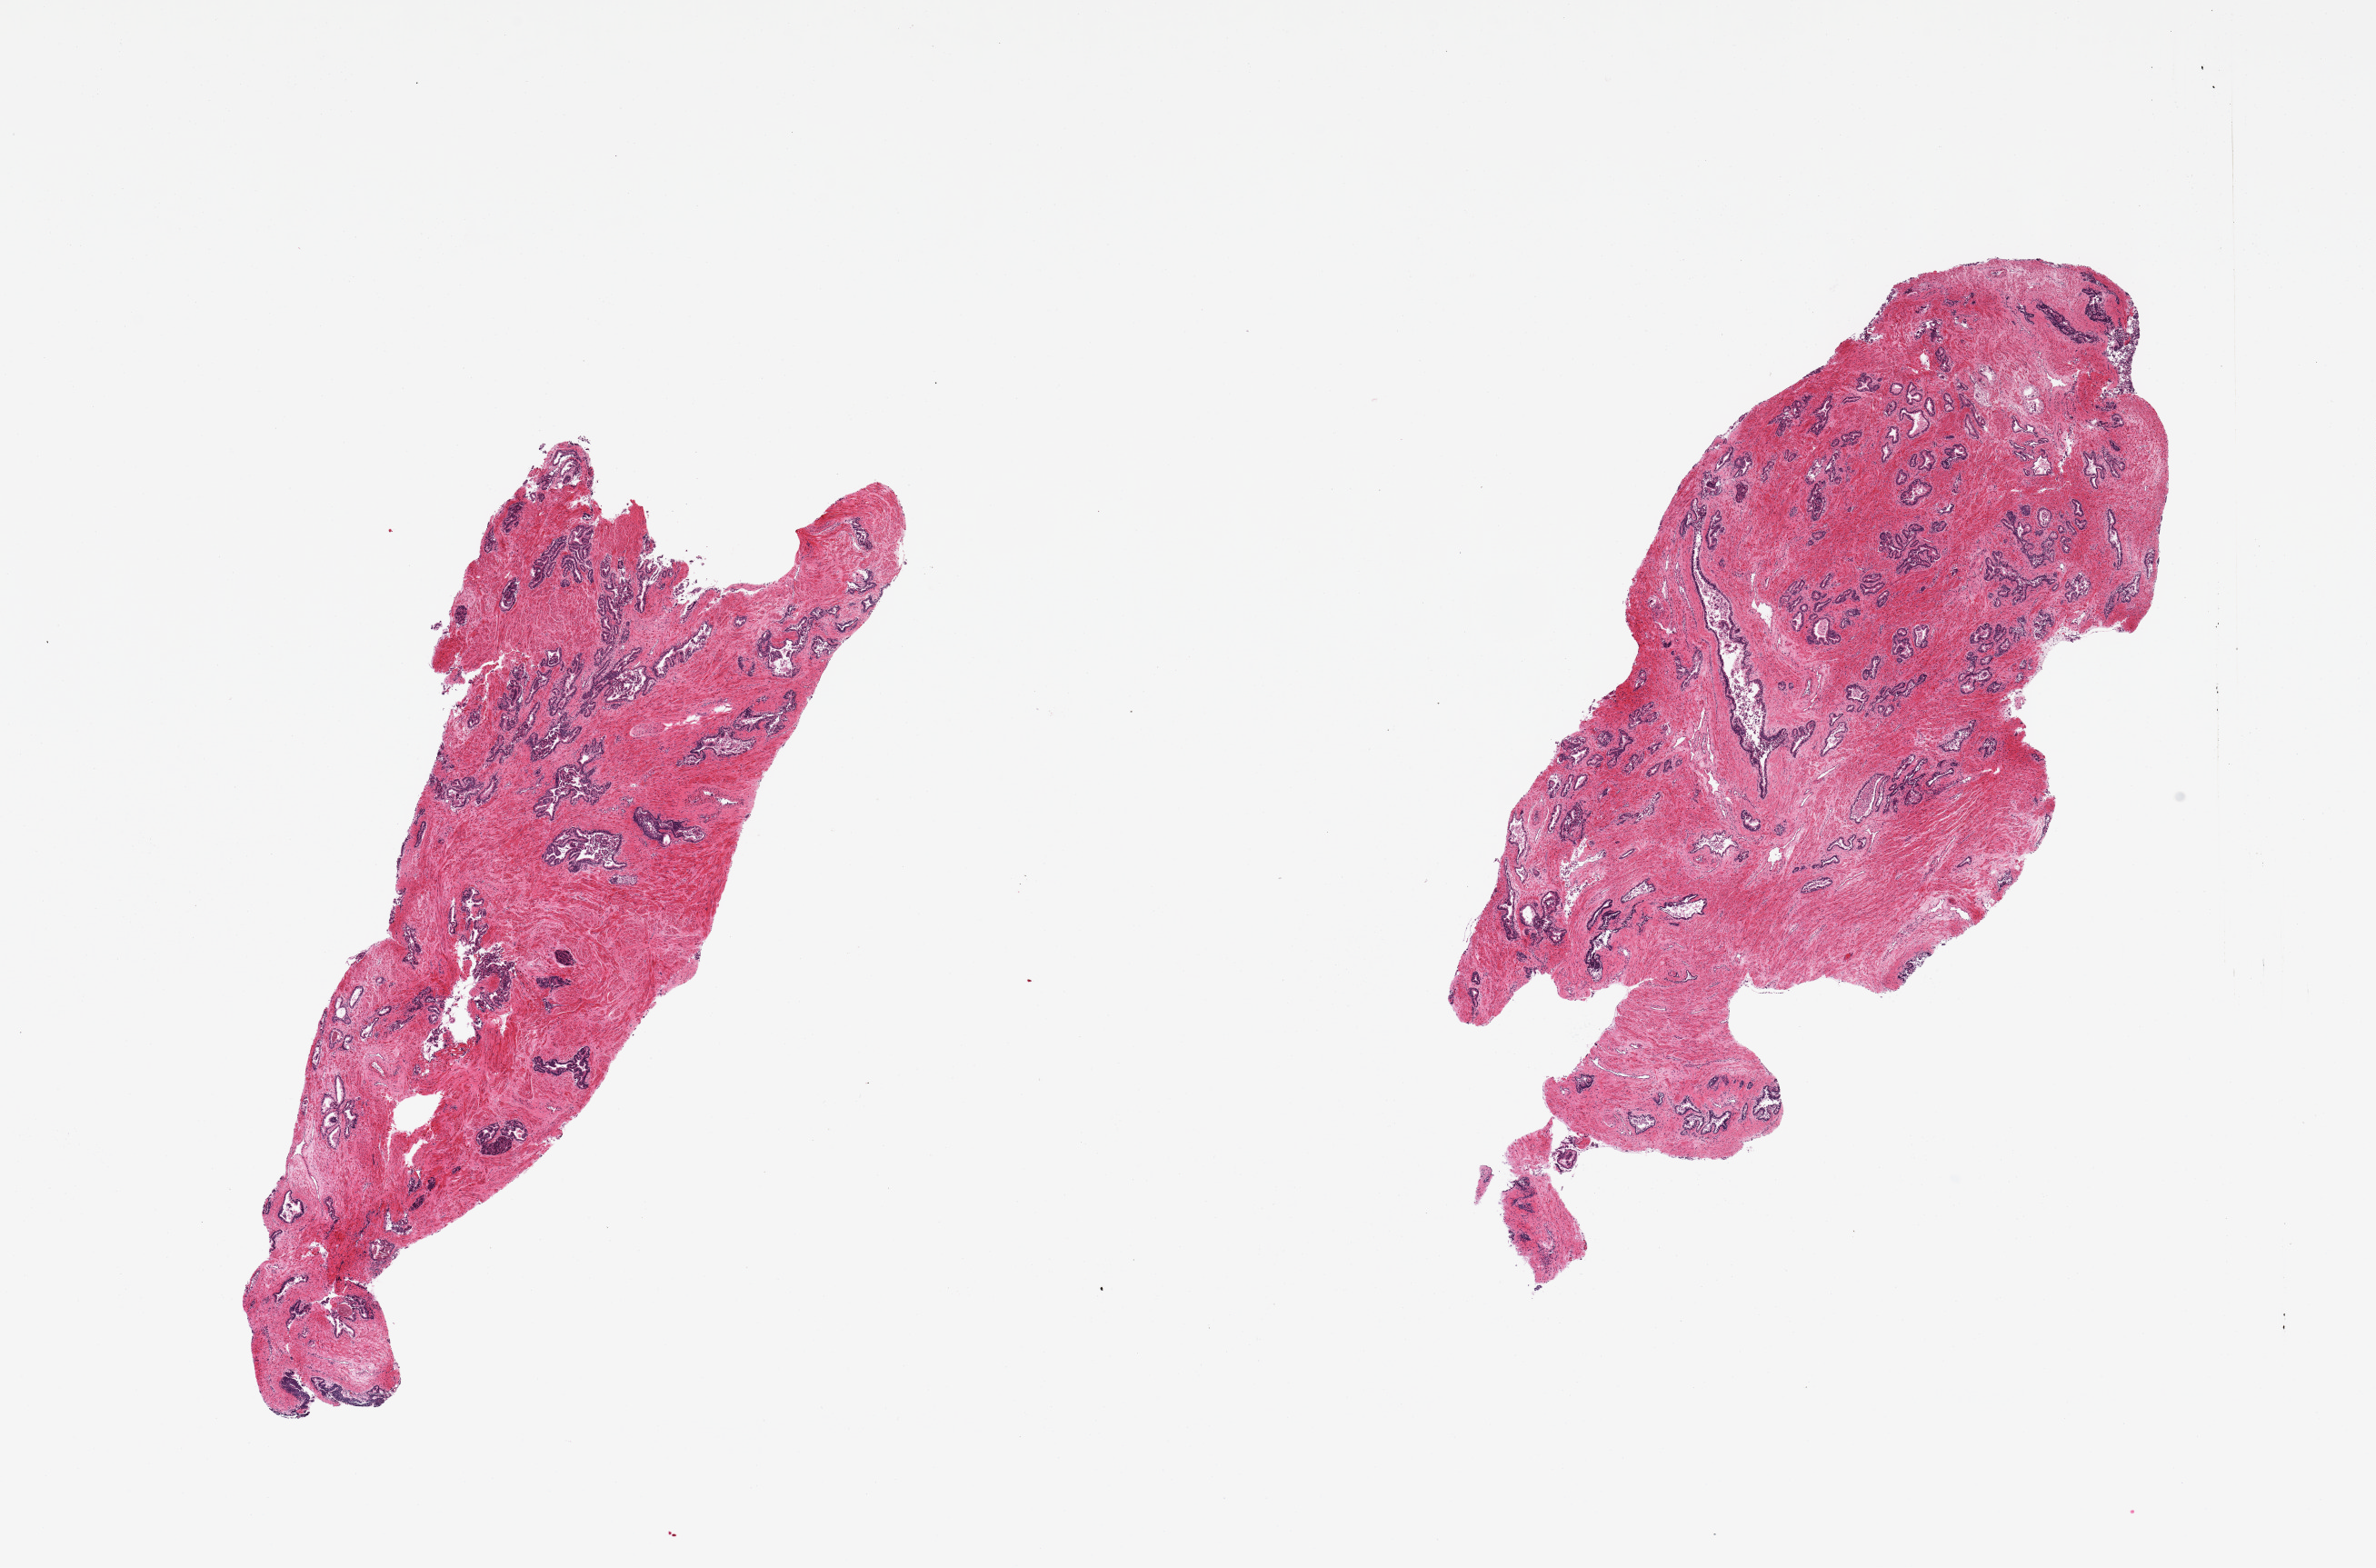
Haematoxylin and eosin whole-slide image, low-resolution overview of the scanned area, about 20.7 x 13.6 mm (acquisition: 20x scan); PAXgene-fixed, paraffin-embedded tissue; section of prostate (target tissue); donor tissue sample. Male donor.
Reviewer comment on this tissue sample: 2 pieces; prostatic urethra at one edge of one piece.